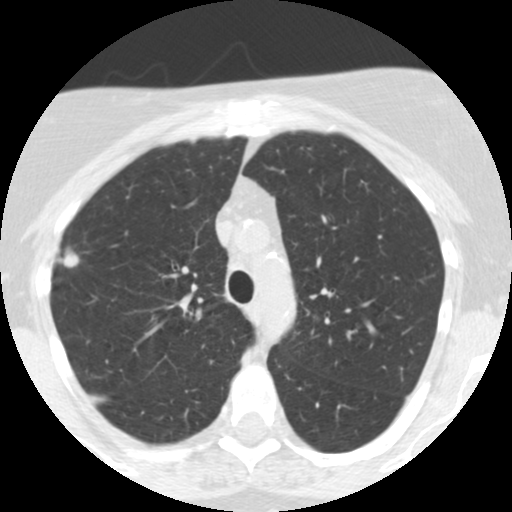
Chest CT (low-dose screening protocol), one axial image; third screening round (two years after baseline); lung window (W 1500 / L -600 HU); 2.5 mm slice thickness; 120 kVp; slice 182 of 248 in the series. Female, age 55 years at enrolment.
Lesion marked by an expert reader, box from (x=48, y=241) to (x=92, y=281) px. The exam's reader record, not a measurement of the box and not confirmed to be the same lesion: non-calcified nodule or mass ≥4 mm, right upper lobe, 10 × 10 mm, poorly defined margins, soft tissue attenuation, pre-existing on the prior screen: yes; interval growth: yes. Lung cancer was diagnosed 145 days after this screen: bronchiolo-alveolar adenocarcinoma, NOS, right upper lobe, moderately differentiated (G2), stage IIA (AJCC 6th edition), 13 mm at pathology.